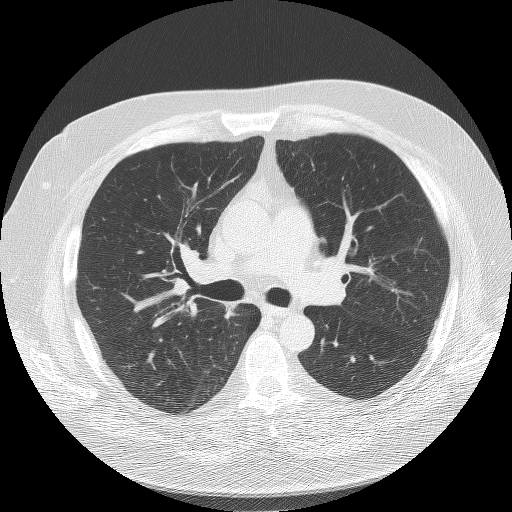
Chest CT (low-dose screening protocol), one axial image, third annual screen, lung window (W 1500 / L -600 HU), lung (sharp) reconstruction kernel (BONE), 120 kVp, 512 × 512 image matrix. Male participant, aged 58 years at enrolment.
Expert-annotated lung lesion, bounding box <190,288,257,341> (left, top, right, bottom; pixels). Screening reader's record for this exam (one nodule recorded; not confirmed to be the boxed lesion): non-calcified nodule or mass ≥4 mm, right upper lobe, 9 × 8 mm, spiculated (stellate) margins, soft tissue attenuation, pre-existing on the prior screen: yes; interval growth: yes. Later outcome: lung cancer diagnosed 157 days after this screen — squamous cell carcinoma, NOS, right upper lobe, moderately differentiated (G2), stage IA (AJCC 6th edition), 18 mm at pathology.